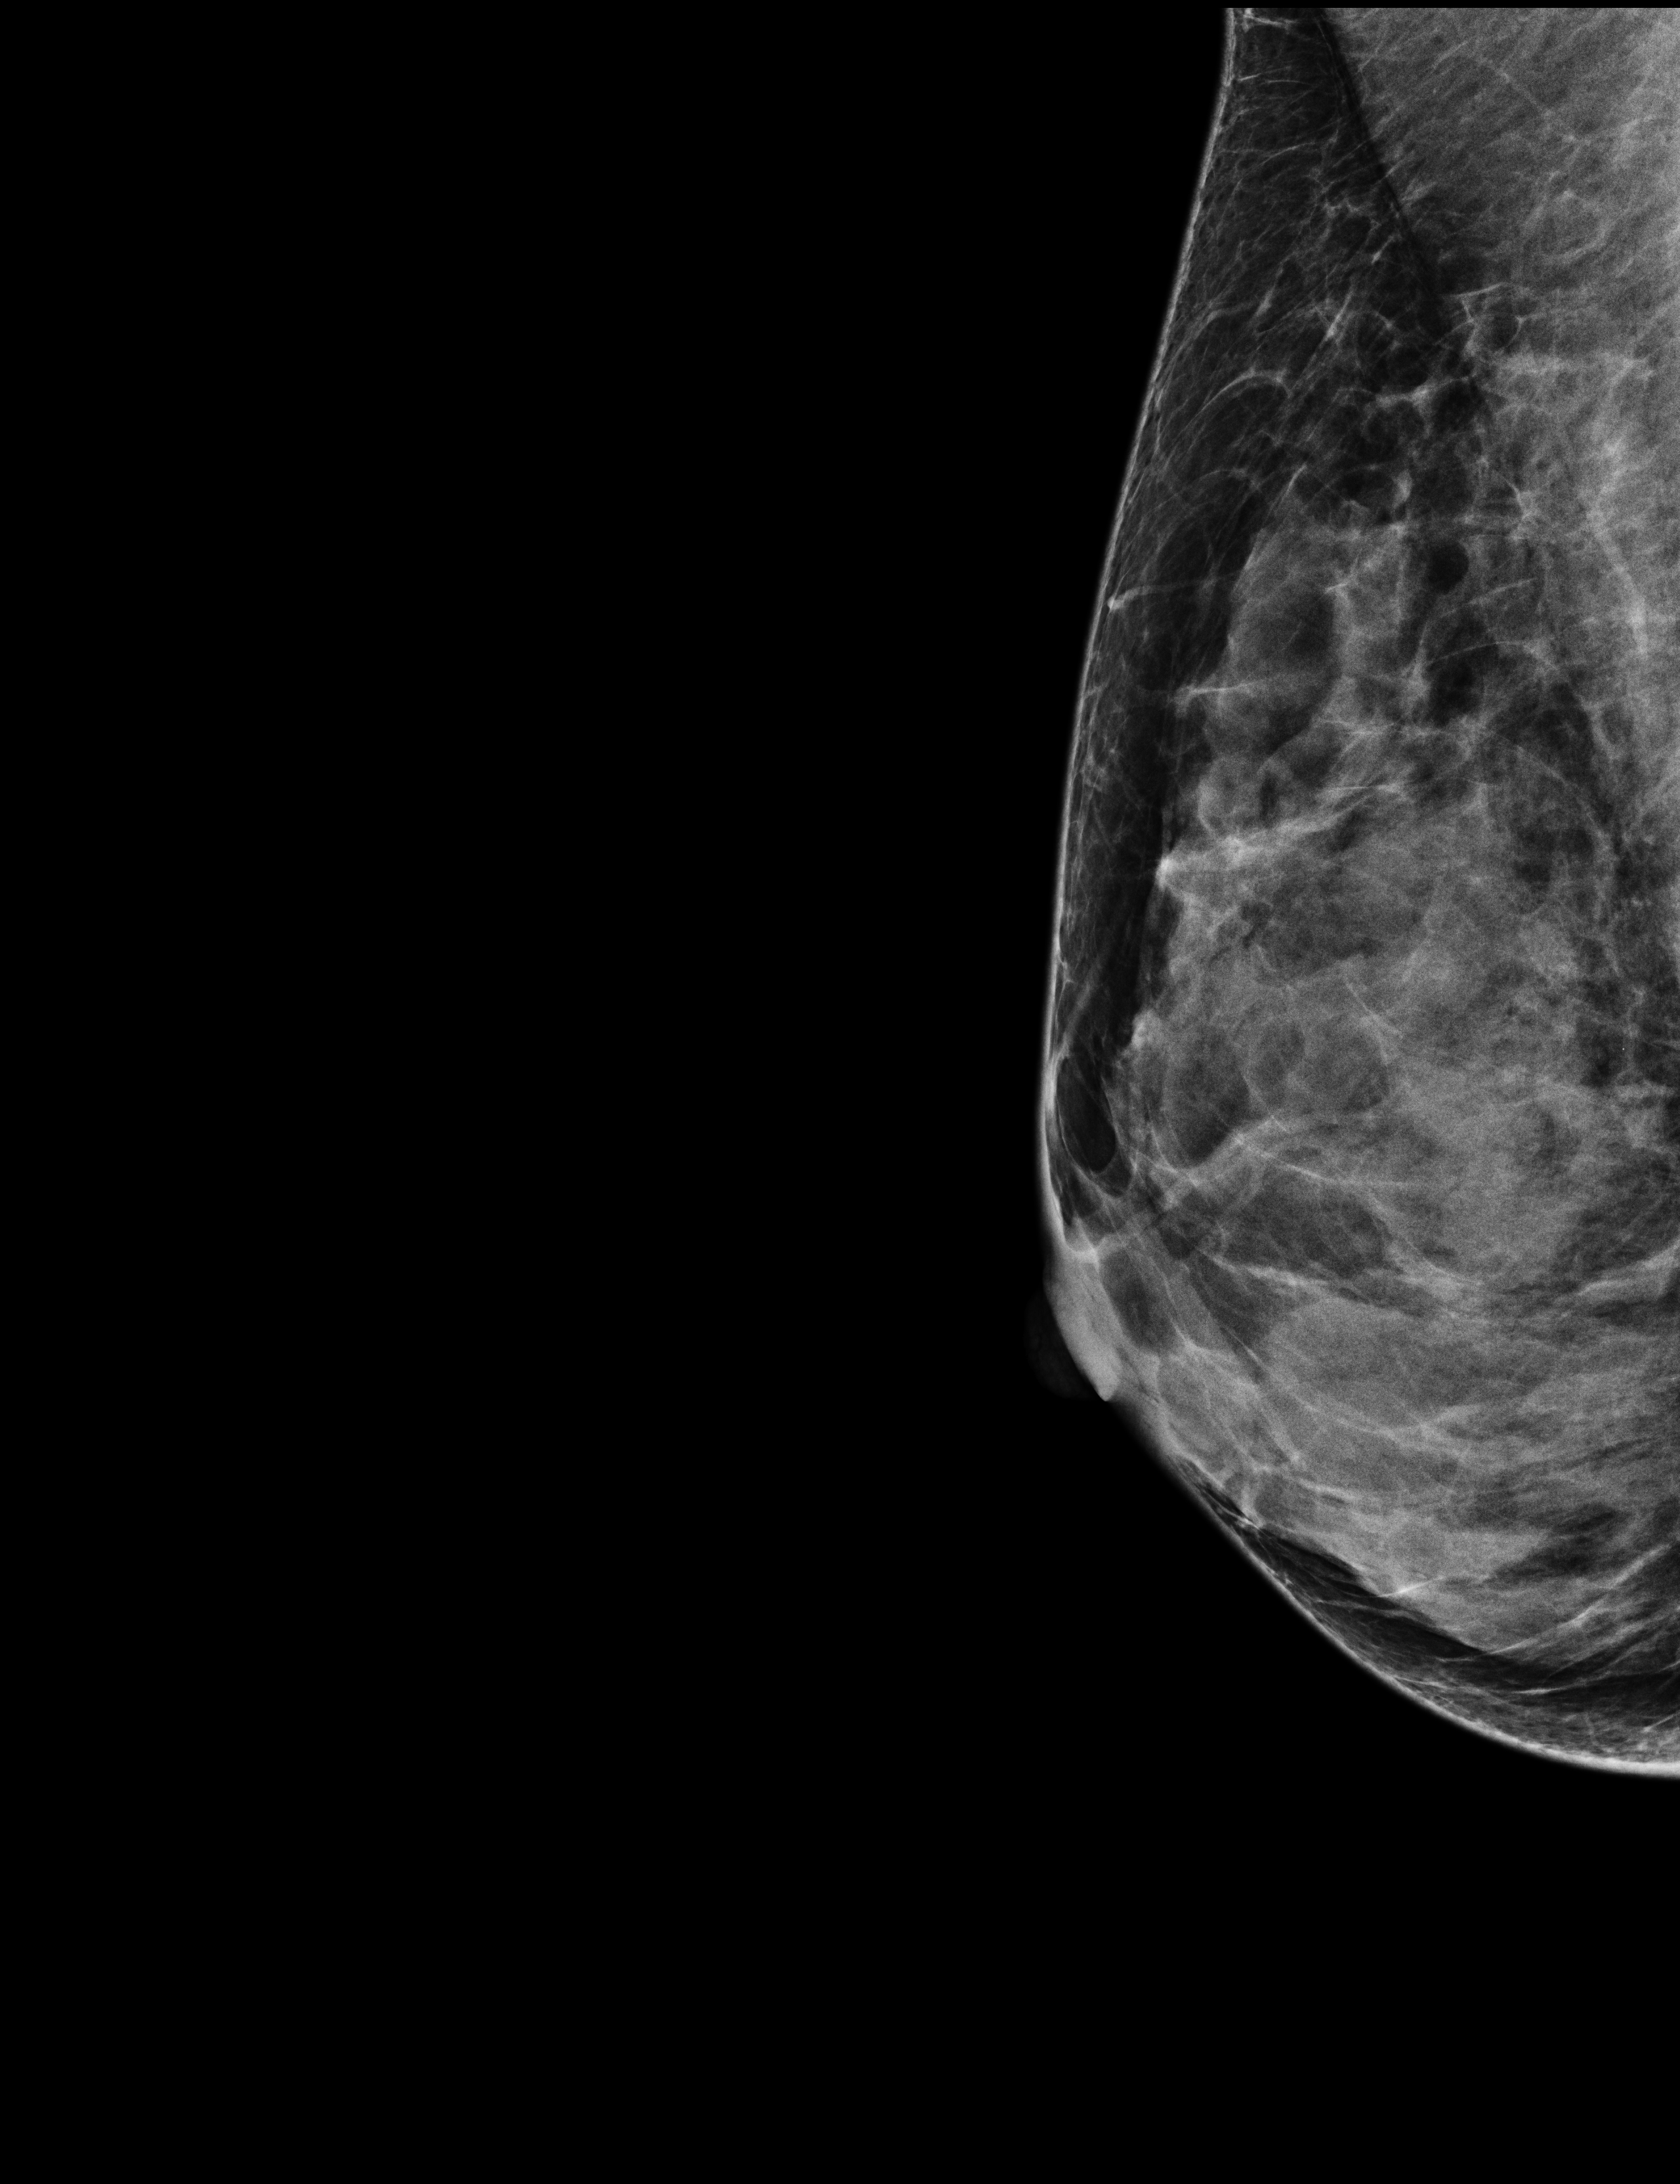
Screening examination, system: Selenia Dimensions. Female patient, age 43 years.
Image type: full-field digital mammogram. Breast: right. Projection: medio-lateral oblique projection.